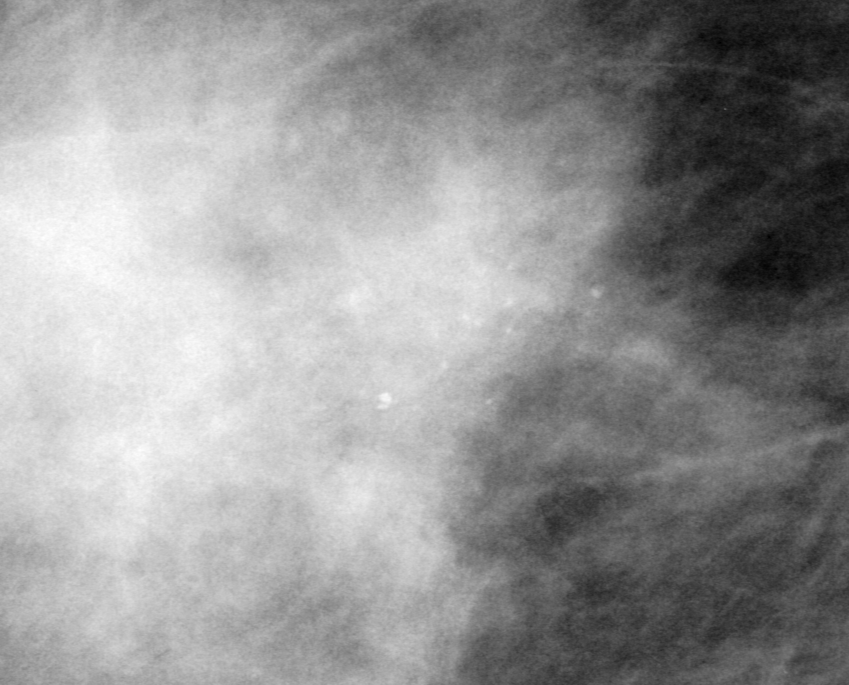
Cropped region of a digitized screen-film mammogram centred on a radiologist-marked abnormality, right breast, MLO view.
Finding: calcifications, morphology pleomorphic, distribution clustered; BI-RADS assessment category 0 (incomplete: needs additional imaging); pathology (as recorded): malignant.